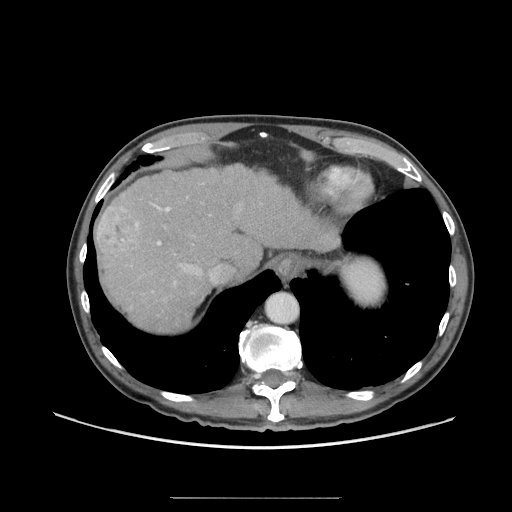
Contrast-enhanced abdominal CT (liver protocol), one axial slice; position 54 of 71 along the scan axis; reconstruction kernel STANDARD; 140 kVp; soft-tissue window (W 400 / L 40 HU); 2.5 mm slice thickness; 512 × 512 image matrix, field of view 400 × 400 mm. Case-level facts recorded for this patient, not image findings: diagnosis: hepatocellular carcinoma (patient treated with transarterial chemoembolisation; whether this scan precedes or follows treatment is not stated here); TNM stage (as recorded): Stage-I; Child-Pugh class: A; tumour differentiation: well differentiated; tumour size: 3.5 cm.
Annotated regions visible in this slice (semi-automatic segmentation, software-assisted and operator-edited):
- abdominal aorta: bounding box <266,294,298,323> (left, top, right, bottom; pixels)
- liver parenchyma outside the tumour (the mass and vessels are separate outlines, so this box may not span the whole liver): <96,164,340,332>
- mass: <96,203,143,261>
- liver vessels: <154,205,214,279>